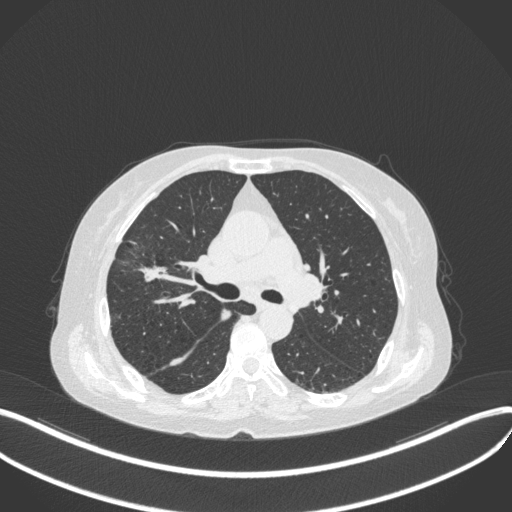
Chest CT, one axial slice. Slice 251 of 429 in the series (ordered by position). Reconstruction kernel B31f. 120 kVp. Lung window (W 1500 / L -600 HU). 1 mm slice thickness. 512 × 512 image matrix. Female patient, age 69 years. From the clinical record (not read from this slice): clinical TNM (as recorded): T1b N3 M0.
Outlined on this slice (bounding box drawn by a radiologist):
- lung tumour (recorded histology: small cell carcinoma): bounding box <133,259,173,286> (left, top, right, bottom; pixels)